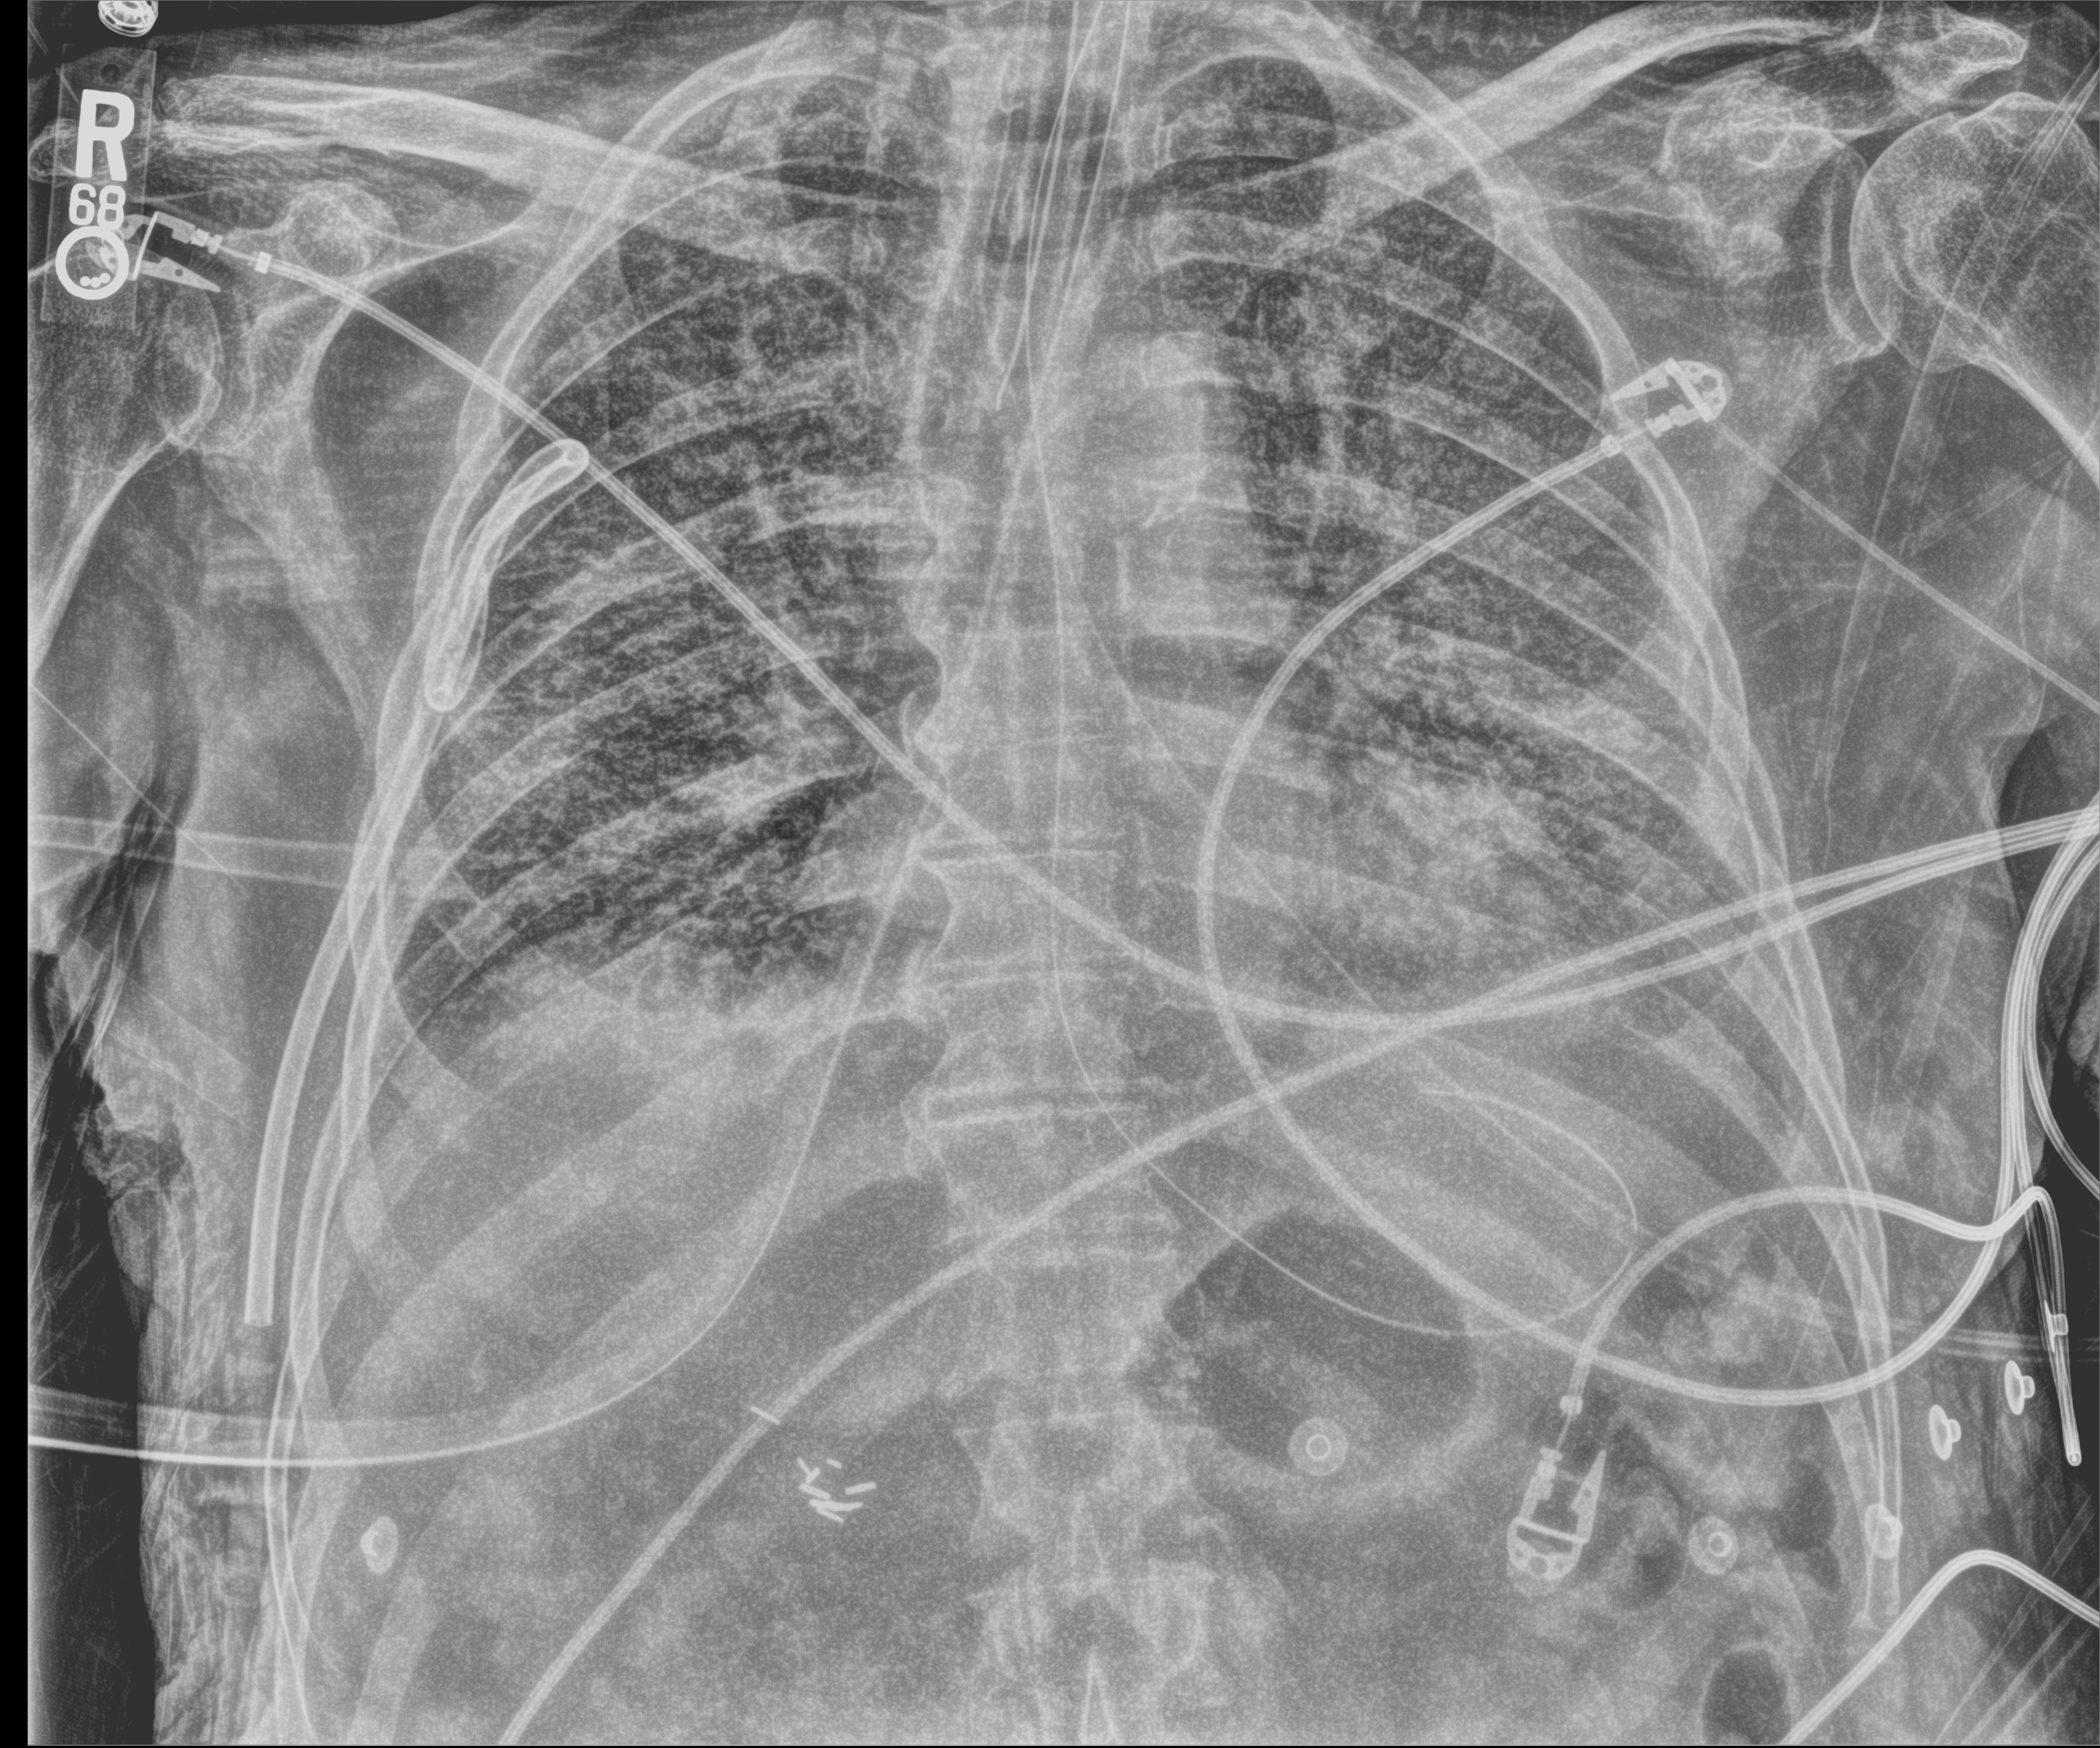
Chest X-ray (portable); anteroposterior (AP) projection. Patient hospitalised with COVID-19; male, aged 75–90 years.
From the hospital-stay record, not from the radiograph (when in the stay this image was taken is not recorded): mechanically ventilated during this hospital stay: yes; admitted to intensive care during this hospital stay: yes.